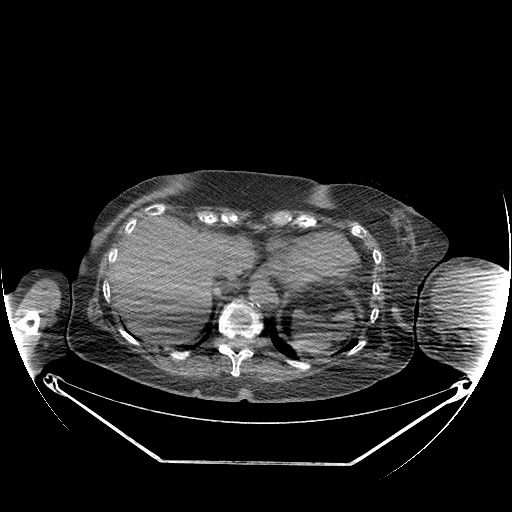
CT of an extremity soft-tissue mass (from a PET/CT study), one axial slice. Slice 141 of 267 in the series (ordered by position). Reconstruction kernel STANDARD. Soft-tissue window (W 400 / L 40 HU). 512 × 512 image matrix, field of view 500 × 500 mm. Female patient. Case-level facts recorded for this patient, not image findings: histological type: pleiomorphic leiomyosarcoma; grade: high; site of the primary tumour: left biceps.
Structures marked on this image (expert contour drawn on MRI and transferred to this co-registered scan by the dataset authors):
- gross tumour volume including surrounding oedema: box from (x=445, y=279) to (x=501, y=321) px
- gross tumour volume (mass): (x=445, y=279)–(x=496, y=303)